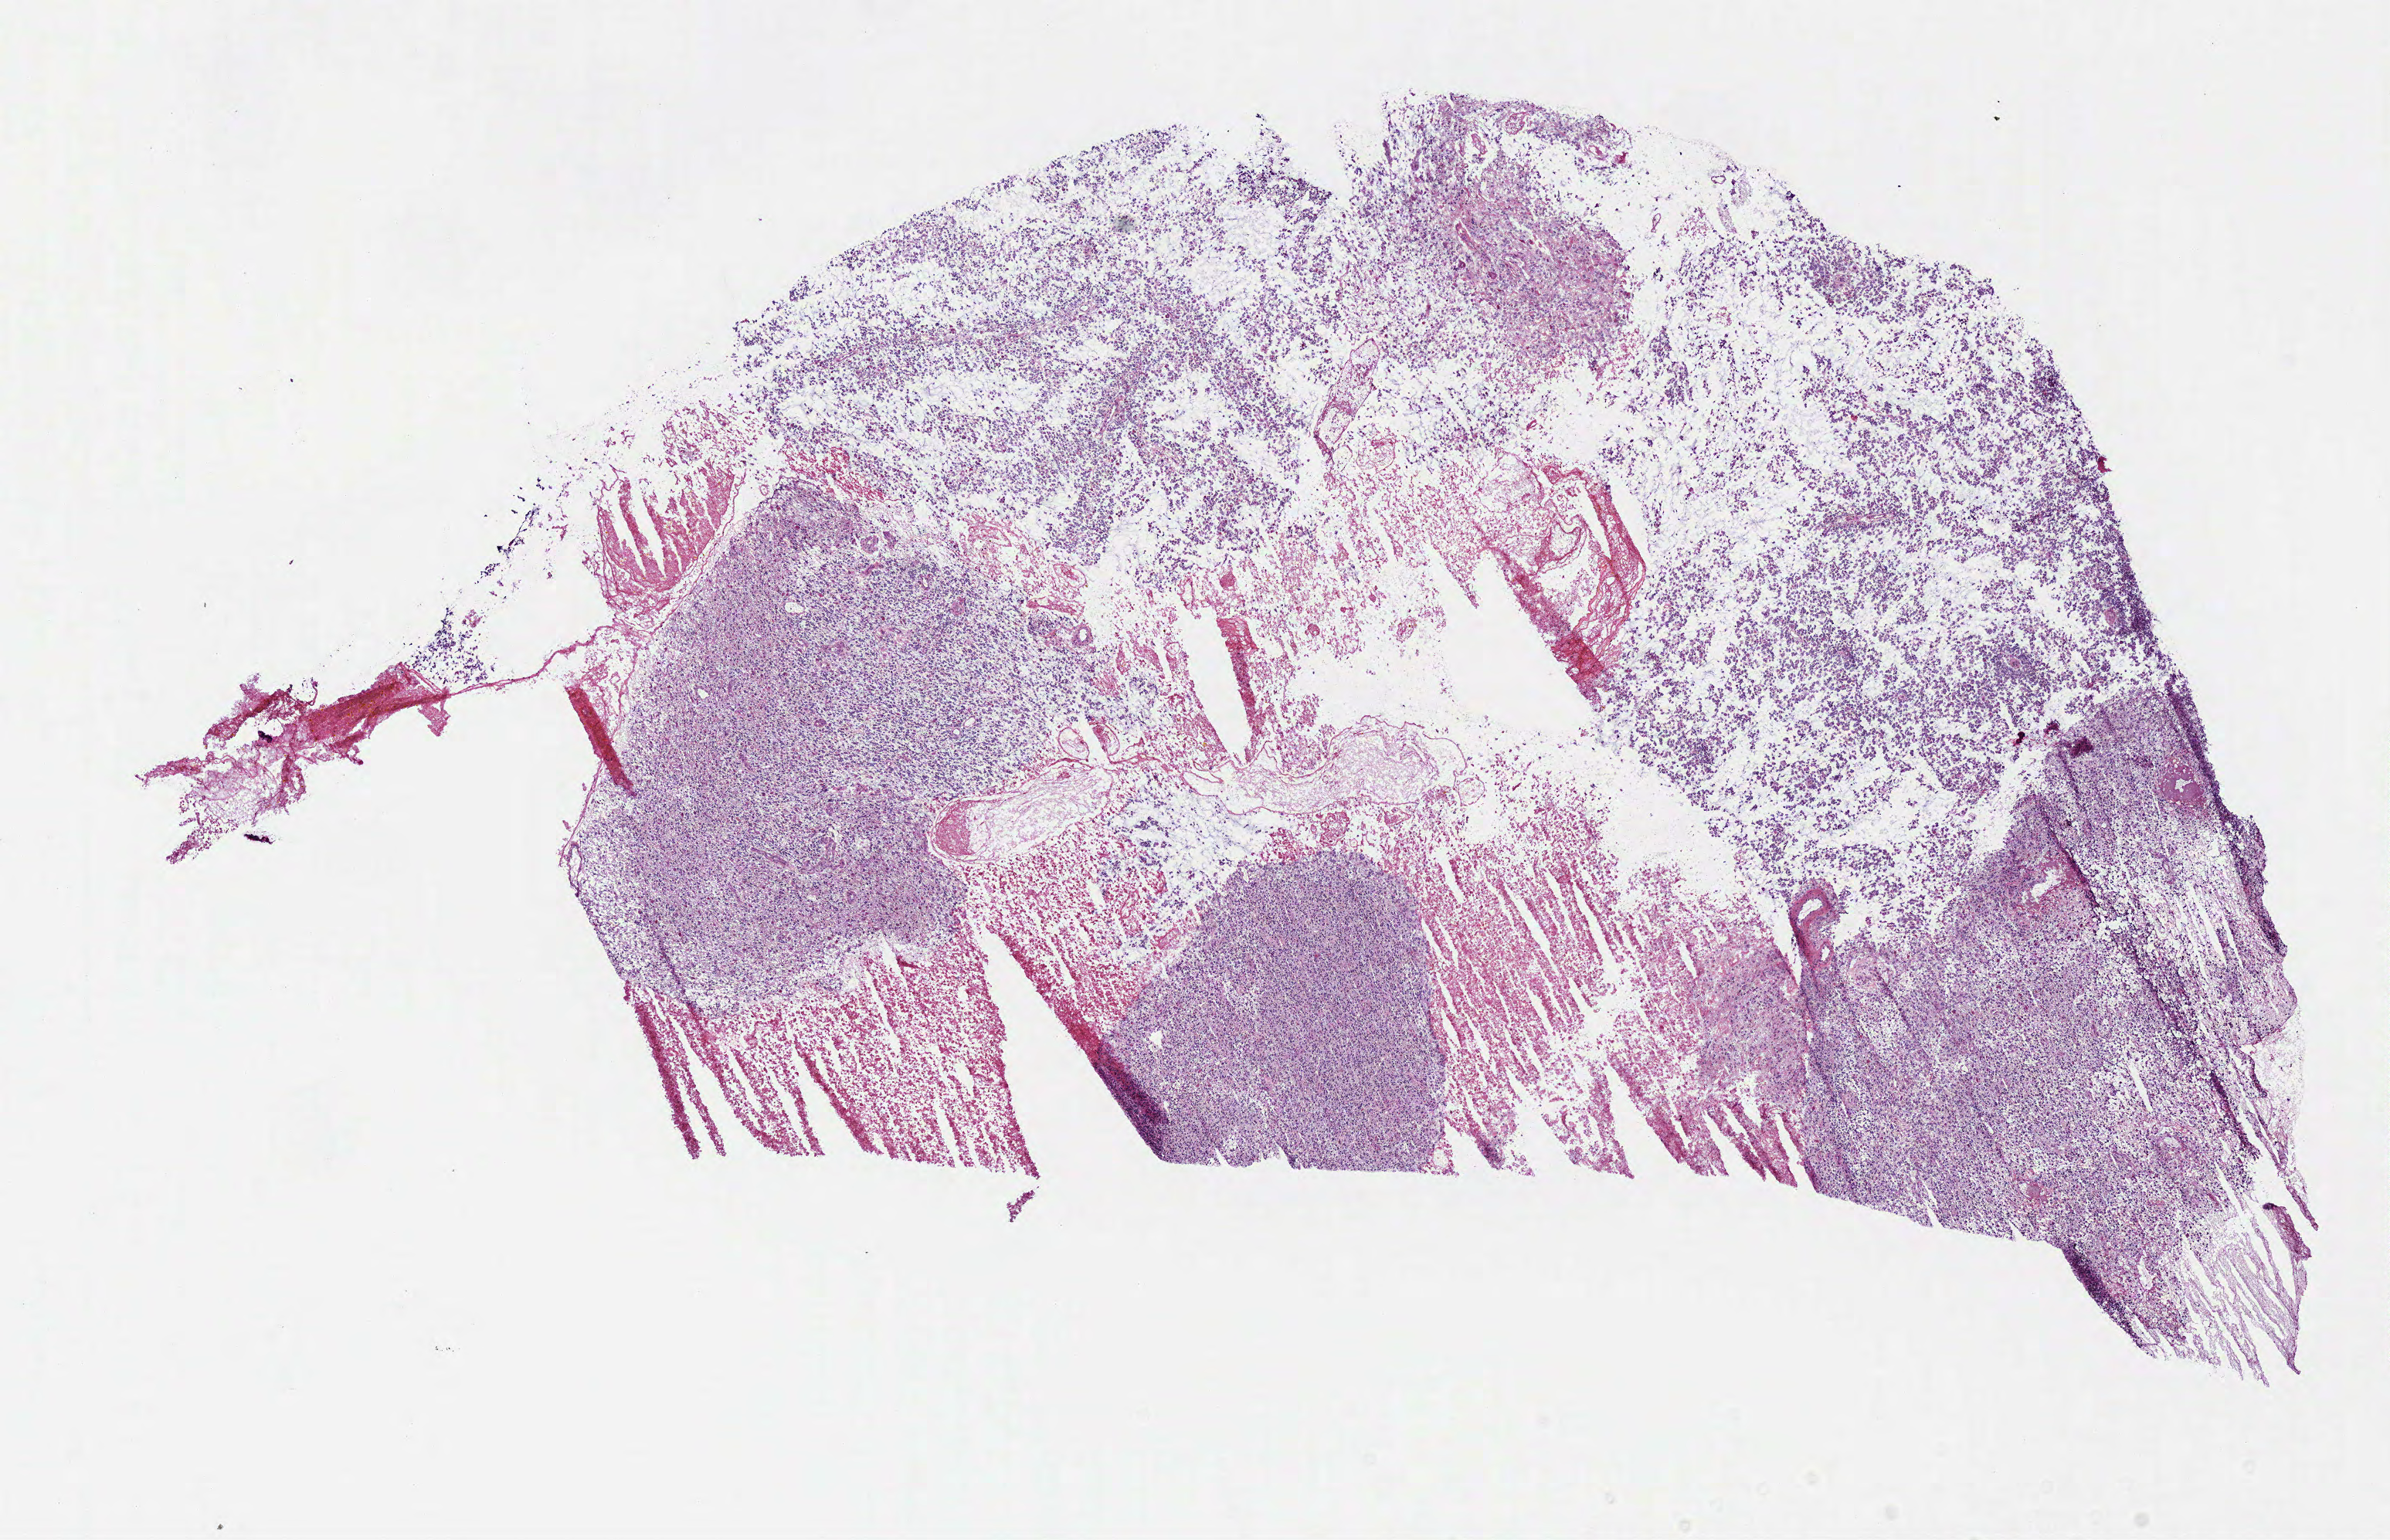
Digitized Hematoxylin and eosin (H&E) stained tissue section (whole slide), shown as a low-resolution overview of the whole scanned area (about 12.2 x 7.9 mm), frozen section from the bottom of the tissue portion, sample: primary tumour, brain. Male patient; age at initial diagnosis 58 years. Pathologist review of this section (percent, as recorded): tumour cells 82%, tumour nuclei 85%, normal cells 0%, stromal cells 0%, necrosis 18%.
Histologic diagnosis: Glioblastoma.